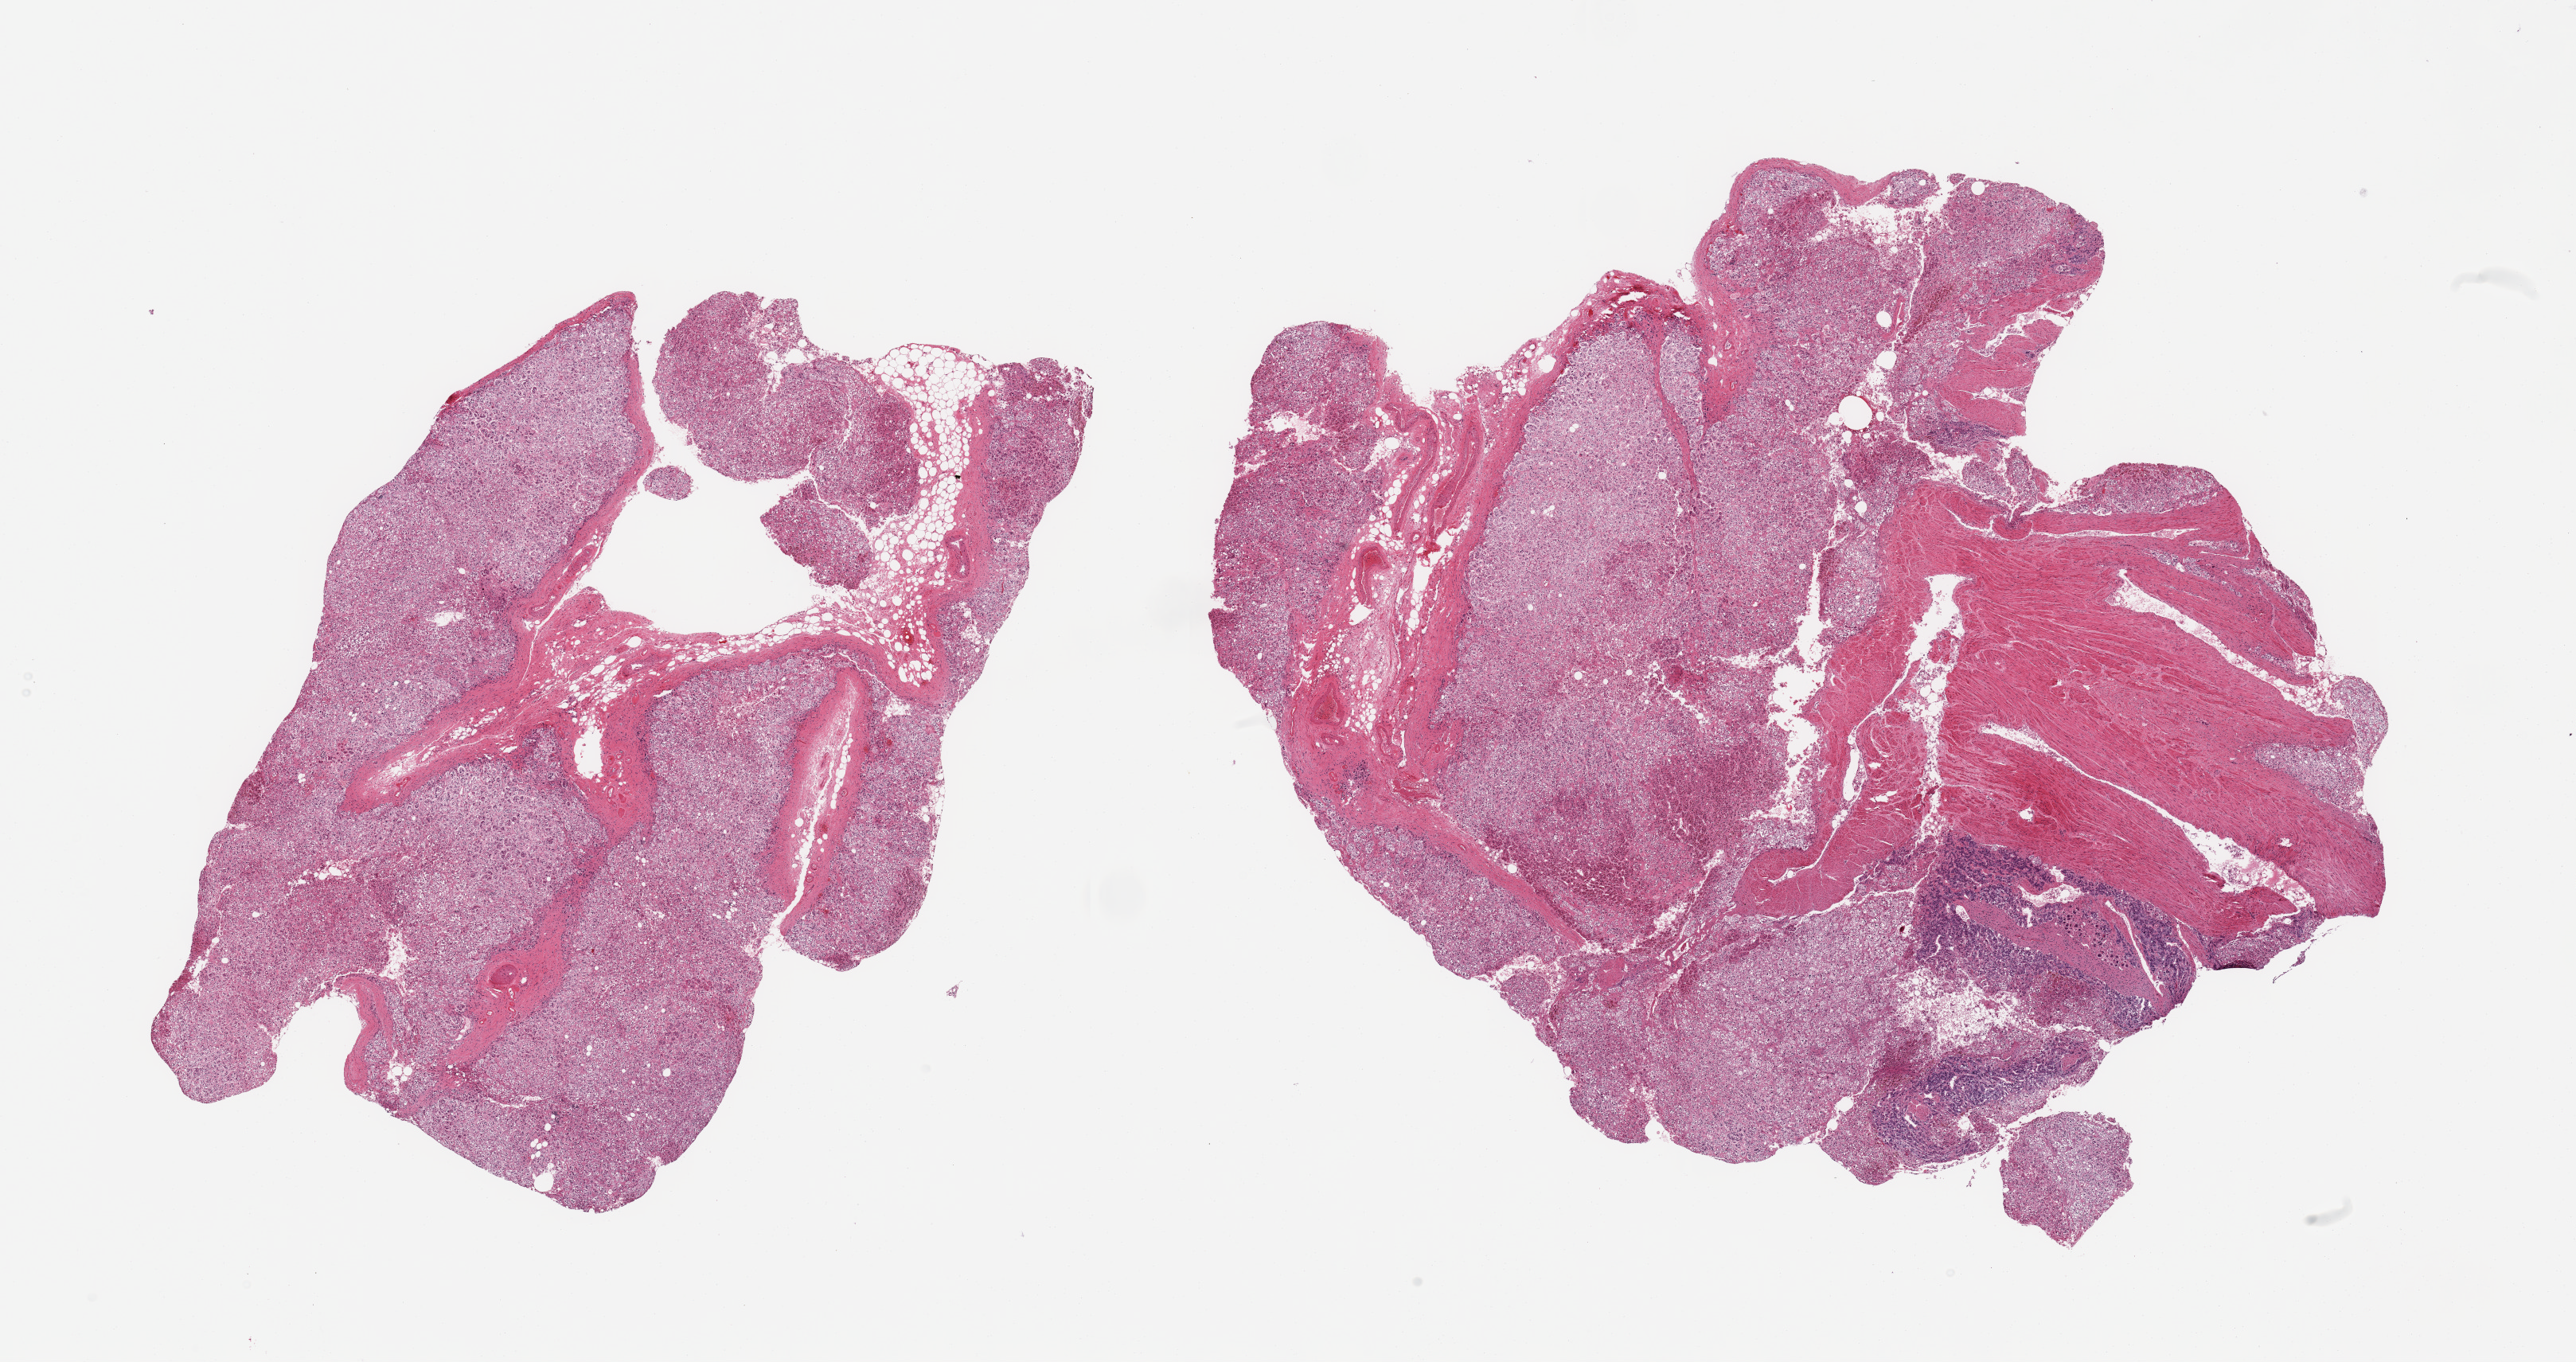
Digitized hematoxylin and eosin (H&E)-stained section, brightfield — a low-resolution overview of the entire scanned area, about 25.6 x 13.5 mm, PAXgene-fixed paraffin-embedded (PFPE) section, target tissue: adrenal gland, donor tissue sample. Male donor.
Pathologist's review note for this sample: 2 pieces; focus of ganglion cells 0.8mm largest diameter; large vessels occupy up to 30% of 1 piece.